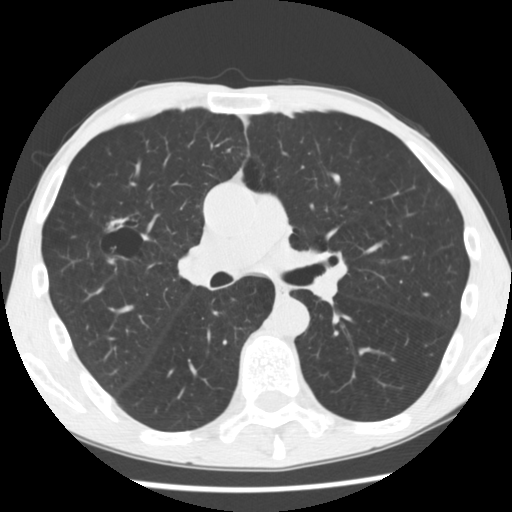
Low-dose screening chest CT, axial slice, first (baseline) screen, lung window (W 1500 / L -600 HU), 2.5 mm slice thickness, slice 130 of 292 in the series, 512 × 512 image matrix, field of view 330 × 330 mm. Male, age 56 years at enrolment. Current smoker at enrolment.
Lesion marked by an expert reader, box from (x=95, y=206) to (x=155, y=258) px. The screening reader recorded 2 non-calcified nodules or masses ≥4 mm on this exam (right upper lobe, right upper lobe); which of them this box marks is not recorded. Official screen result: positive, change unspecified: nodule(s) >= 4 mm or enlarging nodule(s), mass(es), or other non-specific abnormalities suspicious for lung cancer. Participant outcome: lung cancer diagnosed 476 days after this screen (after the second annual screen) — squamous cell carcinoma, NOS, right upper lobe, right middle lobe, well differentiated (G1), stage IA (AJCC 6th edition), 27 mm at pathology.